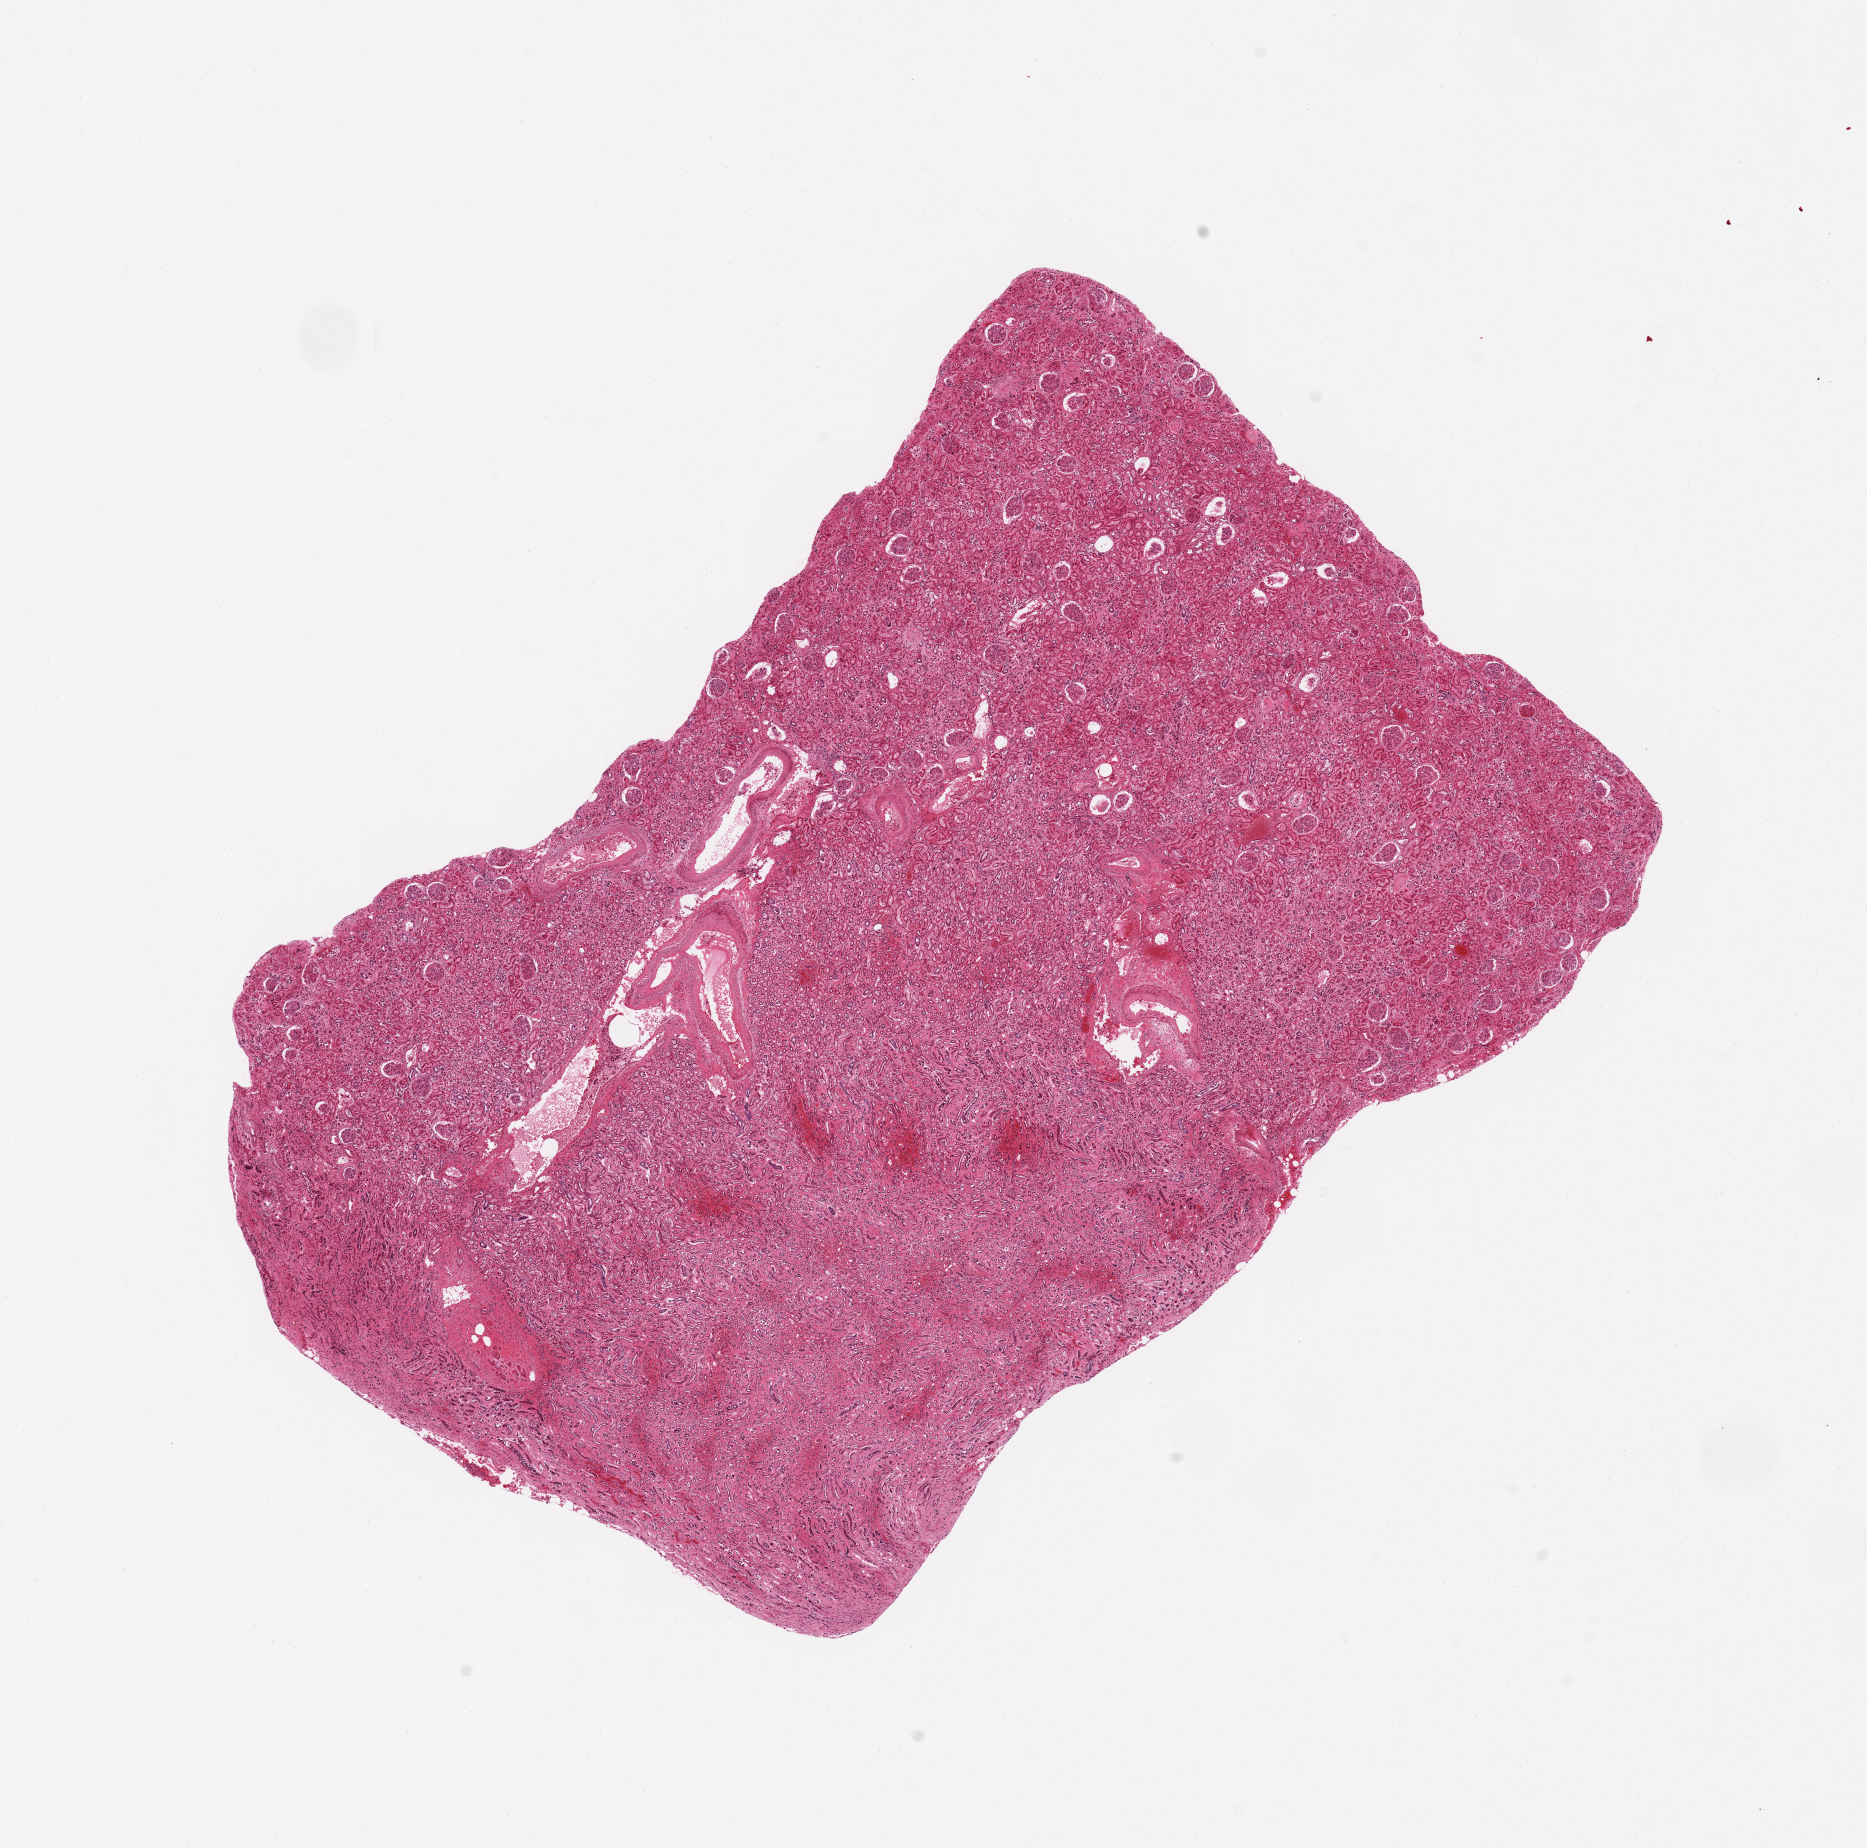
Whole-slide image, haematoxylin and eosin stain — a low-resolution overview of the entire scanned area, about 14.8 x 14.6 mm; PAXgene-fixed paraffin-embedded (PFPE) section; section of renal medulla (target tissue); donor tissue sample. Donor sex: female.
Pathologist's review note for this sample: 10x6.3mm. Approximately 60% contains glomeruli (cortex). Area under ovals is pure tubules.